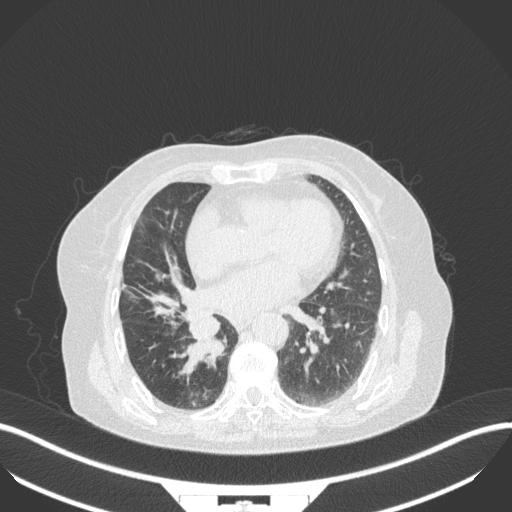
Chest CT, one axial slice; slice 135 of 329 in the series (ordered by position); 120 kVp; lung window (W 1500 / L -600 HU); 1 mm slice thickness; 512 × 512 image matrix, field of view 400 × 400 mm. Patient: female, 75 years. Case-level facts recorded for this patient, not image findings: clinical TNM (as recorded): T1b N0 M1a; histopathological grade: G1.
Structures marked on this image (rectangle marked by the reading radiologist):
- lung tumour (recorded histology: squamous cell carcinoma): box from (x=175, y=316) to (x=225, y=374) px